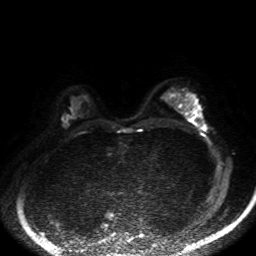
Breast MRI, one axial slice; position 31 of 50 along the scan axis; diffusion-weighted series; image 2 of 4 stored at this slice position (different b-values; order by instance number); 1.5 T; 4 mm slice thickness; 256 × 256 image matrix, field of view 320 × 320 mm. Female patient.
Outlined on this slice (manually delineated by an expert):
- tumour on diffusion-weighted imaging: bounding box <191,120,198,126> (left, top, right, bottom; pixels)